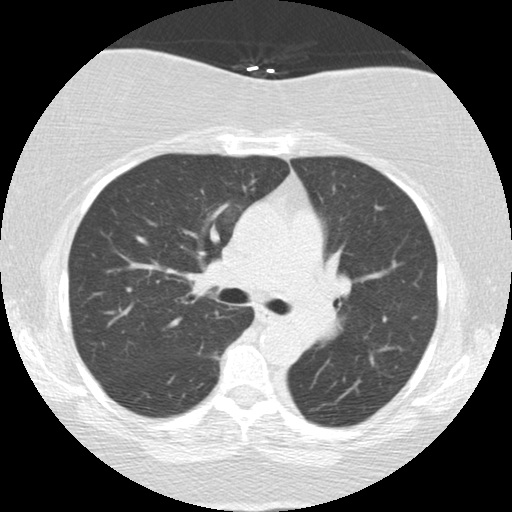
Low-dose screening chest CT, one axial slice. Slice 84 of 136 in the series (ordered by position). Reconstruction kernel STANDARD. 120 kVp. Lung window (W 1500 / L -600 HU). 512 × 512 image matrix, field of view 309 × 309 mm.
Annotated regions visible in this slice (expert manual segmentation):
- lesion 2 (tumor, mediastinum): box from (x=284, y=269) to (x=351, y=343) px